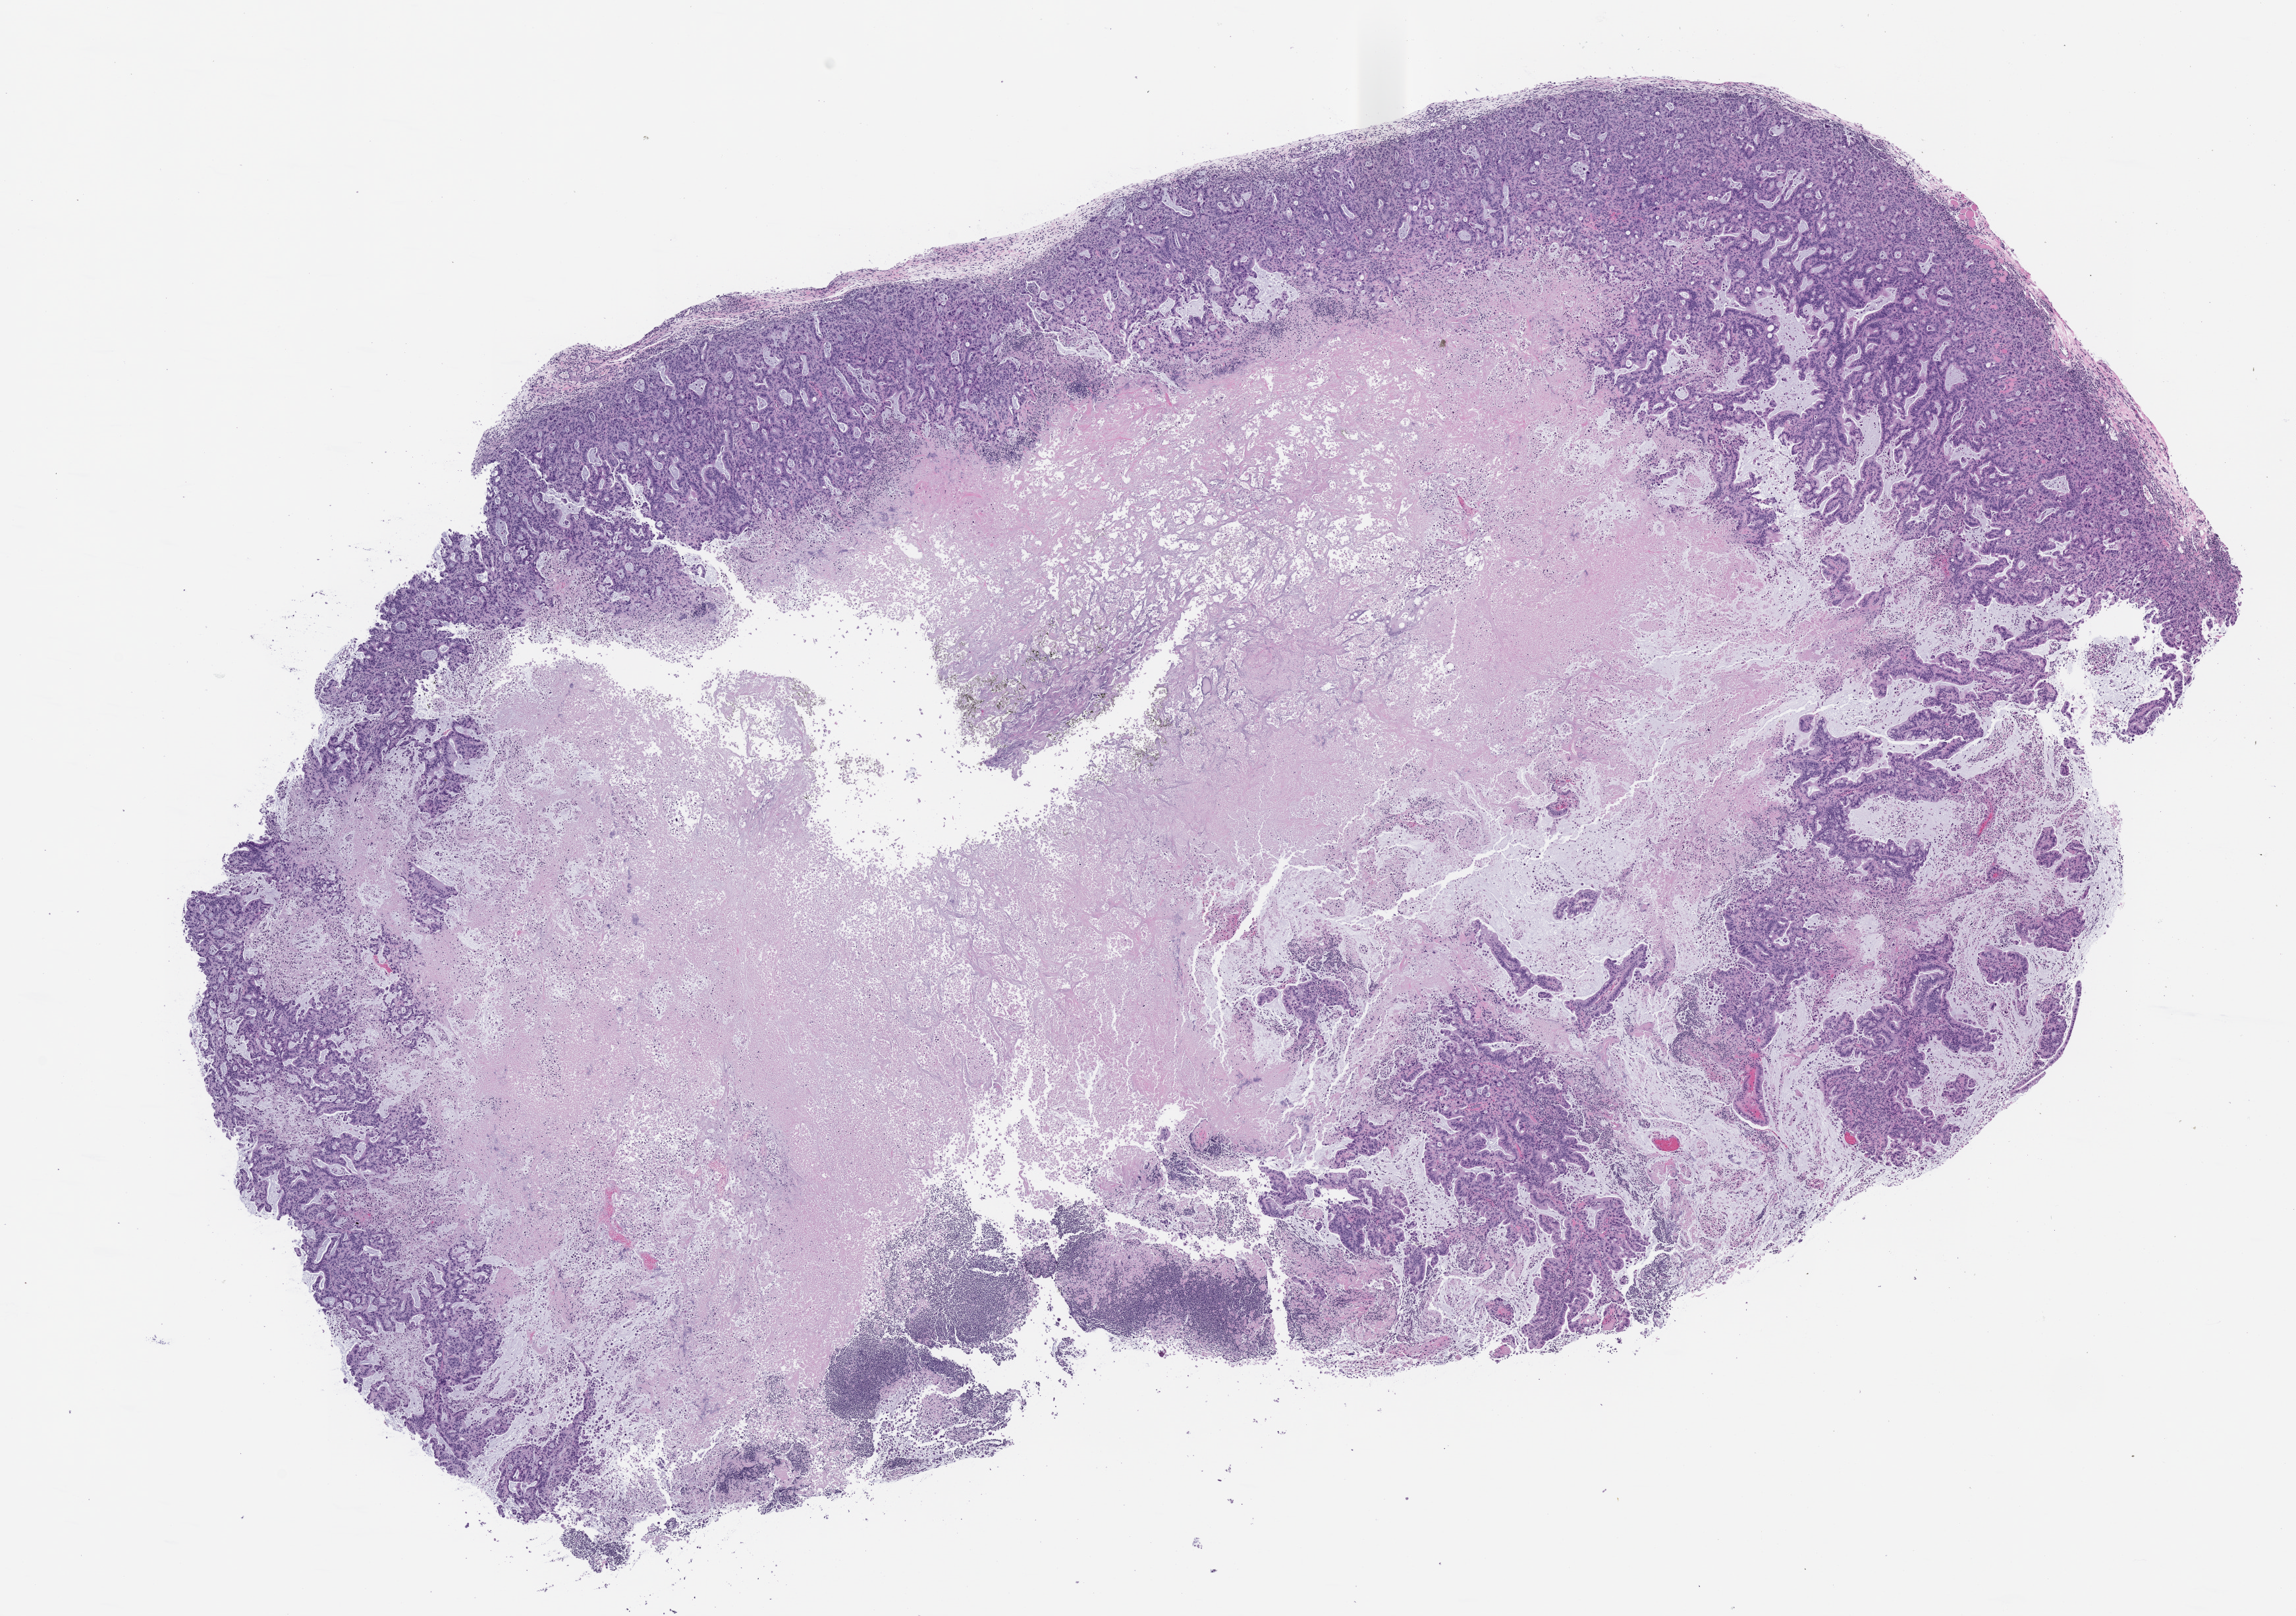
Whole-slide image, H&E: patient-derived xenograft (human tumor grown in a mouse), passage 2 — low-resolution overview of the scanned area, about 14.0 x 9.9 mm; formalin-fixed, paraffin-embedded (FFPE) tissue; tumor site category: pancreas.
- originating patient diagnosis: Pancreatic Adenocarcinoma